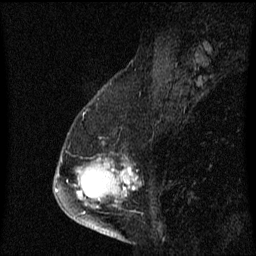
Breast MRI (dynamic contrast-enhanced), one sagittal slice. Position 25 of 60 along the scan axis. Dynamic contrast-enhanced series, image 2 of 3 at this slice position (ordered by acquisition). 1.5 T. TE 4.2 ms, TR 8.4 ms. 256 × 256 image matrix, field of view 200 × 200 mm. Patient: female, 57 years. Case-level facts recorded for this patient, not image findings: setting: breast cancer imaged before/during neoadjuvant chemotherapy; receptor status: HR-positive, HER2-negative.
Outlined on this slice (semi-automatically segmented with operator editing):
- analysis volume of interest (the breast-tissue region the enhancement analysis was run in; not a lesion): bounding box (x1, y1, x2, y2) in pixels: (75, 142, 129, 177)
- tumour enhancement mask (voxels above the 70 % enhancement threshold inside the analysis volume of interest): (112, 168, 129, 173)